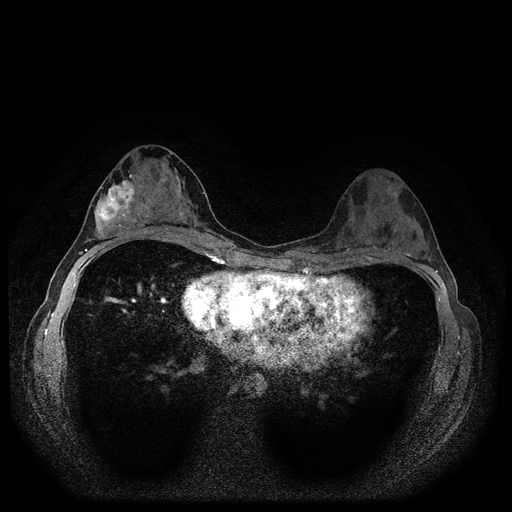
Breast MRI (dynamic contrast-enhanced, multi-phase), one axial slice. Position 55 of 116 along the scan axis. Dynamic contrast-enhanced series, time point 2 of 5 at this slice position (early post-contrast). 1.5 T. TE 2.7 ms, TR 5.4 ms. 2 mm slice thickness. 512 × 512 image matrix. Patient: female, 29 years.
Annotated regions visible in this slice (semi-automatically segmented with operator editing):
- breast lesion (labelled 'tumour' in the annotation; benign lesions carry a separate 'benign' label): bounding box [x1, y1, x2, y2] px = [94, 174, 137, 240]